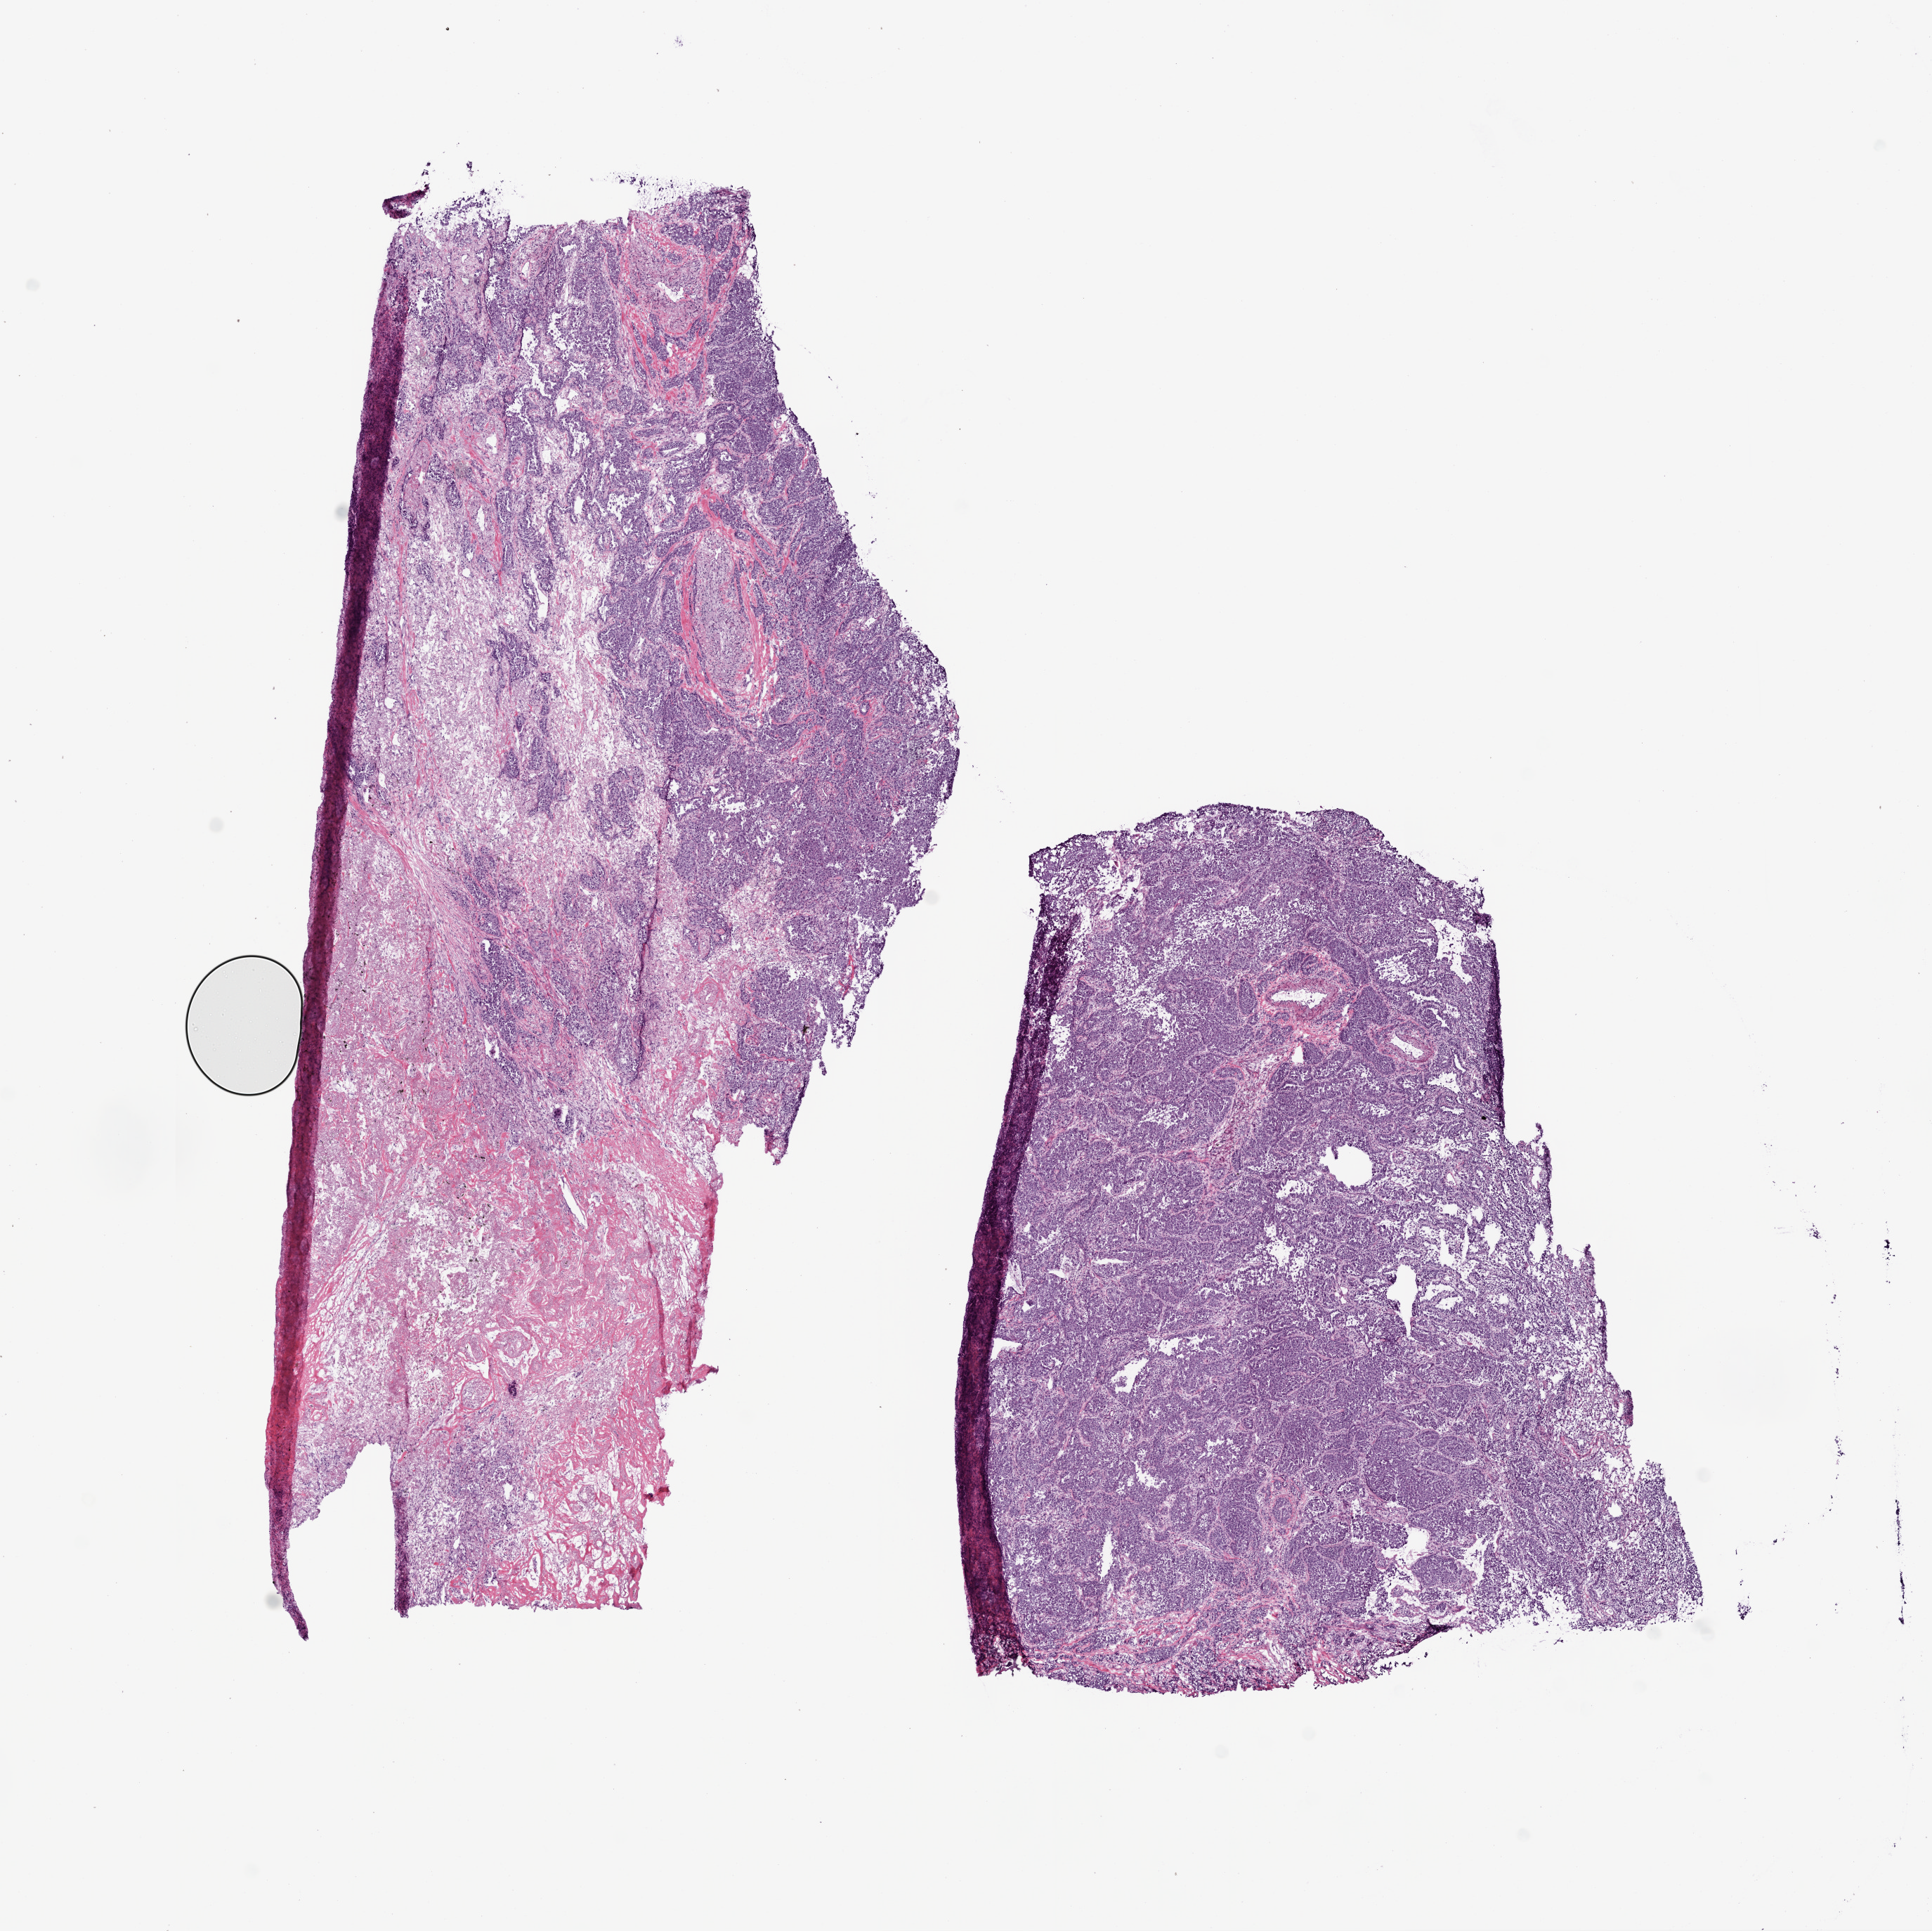
H&E whole-slide image — shown as a low-resolution overview of the whole scanned area (about 11.0 x 11.0 mm, acquisition: 20x scan). Frozen section from the bottom of the tissue portion. Lung, primary tumour sample. Male, age 57 years at initial diagnosis. Pathologist review of this section (percent, as recorded): tumour cells 80%, tumour nuclei 85%.
Diagnosis: Adenocarcinoma with mixed subtypes.